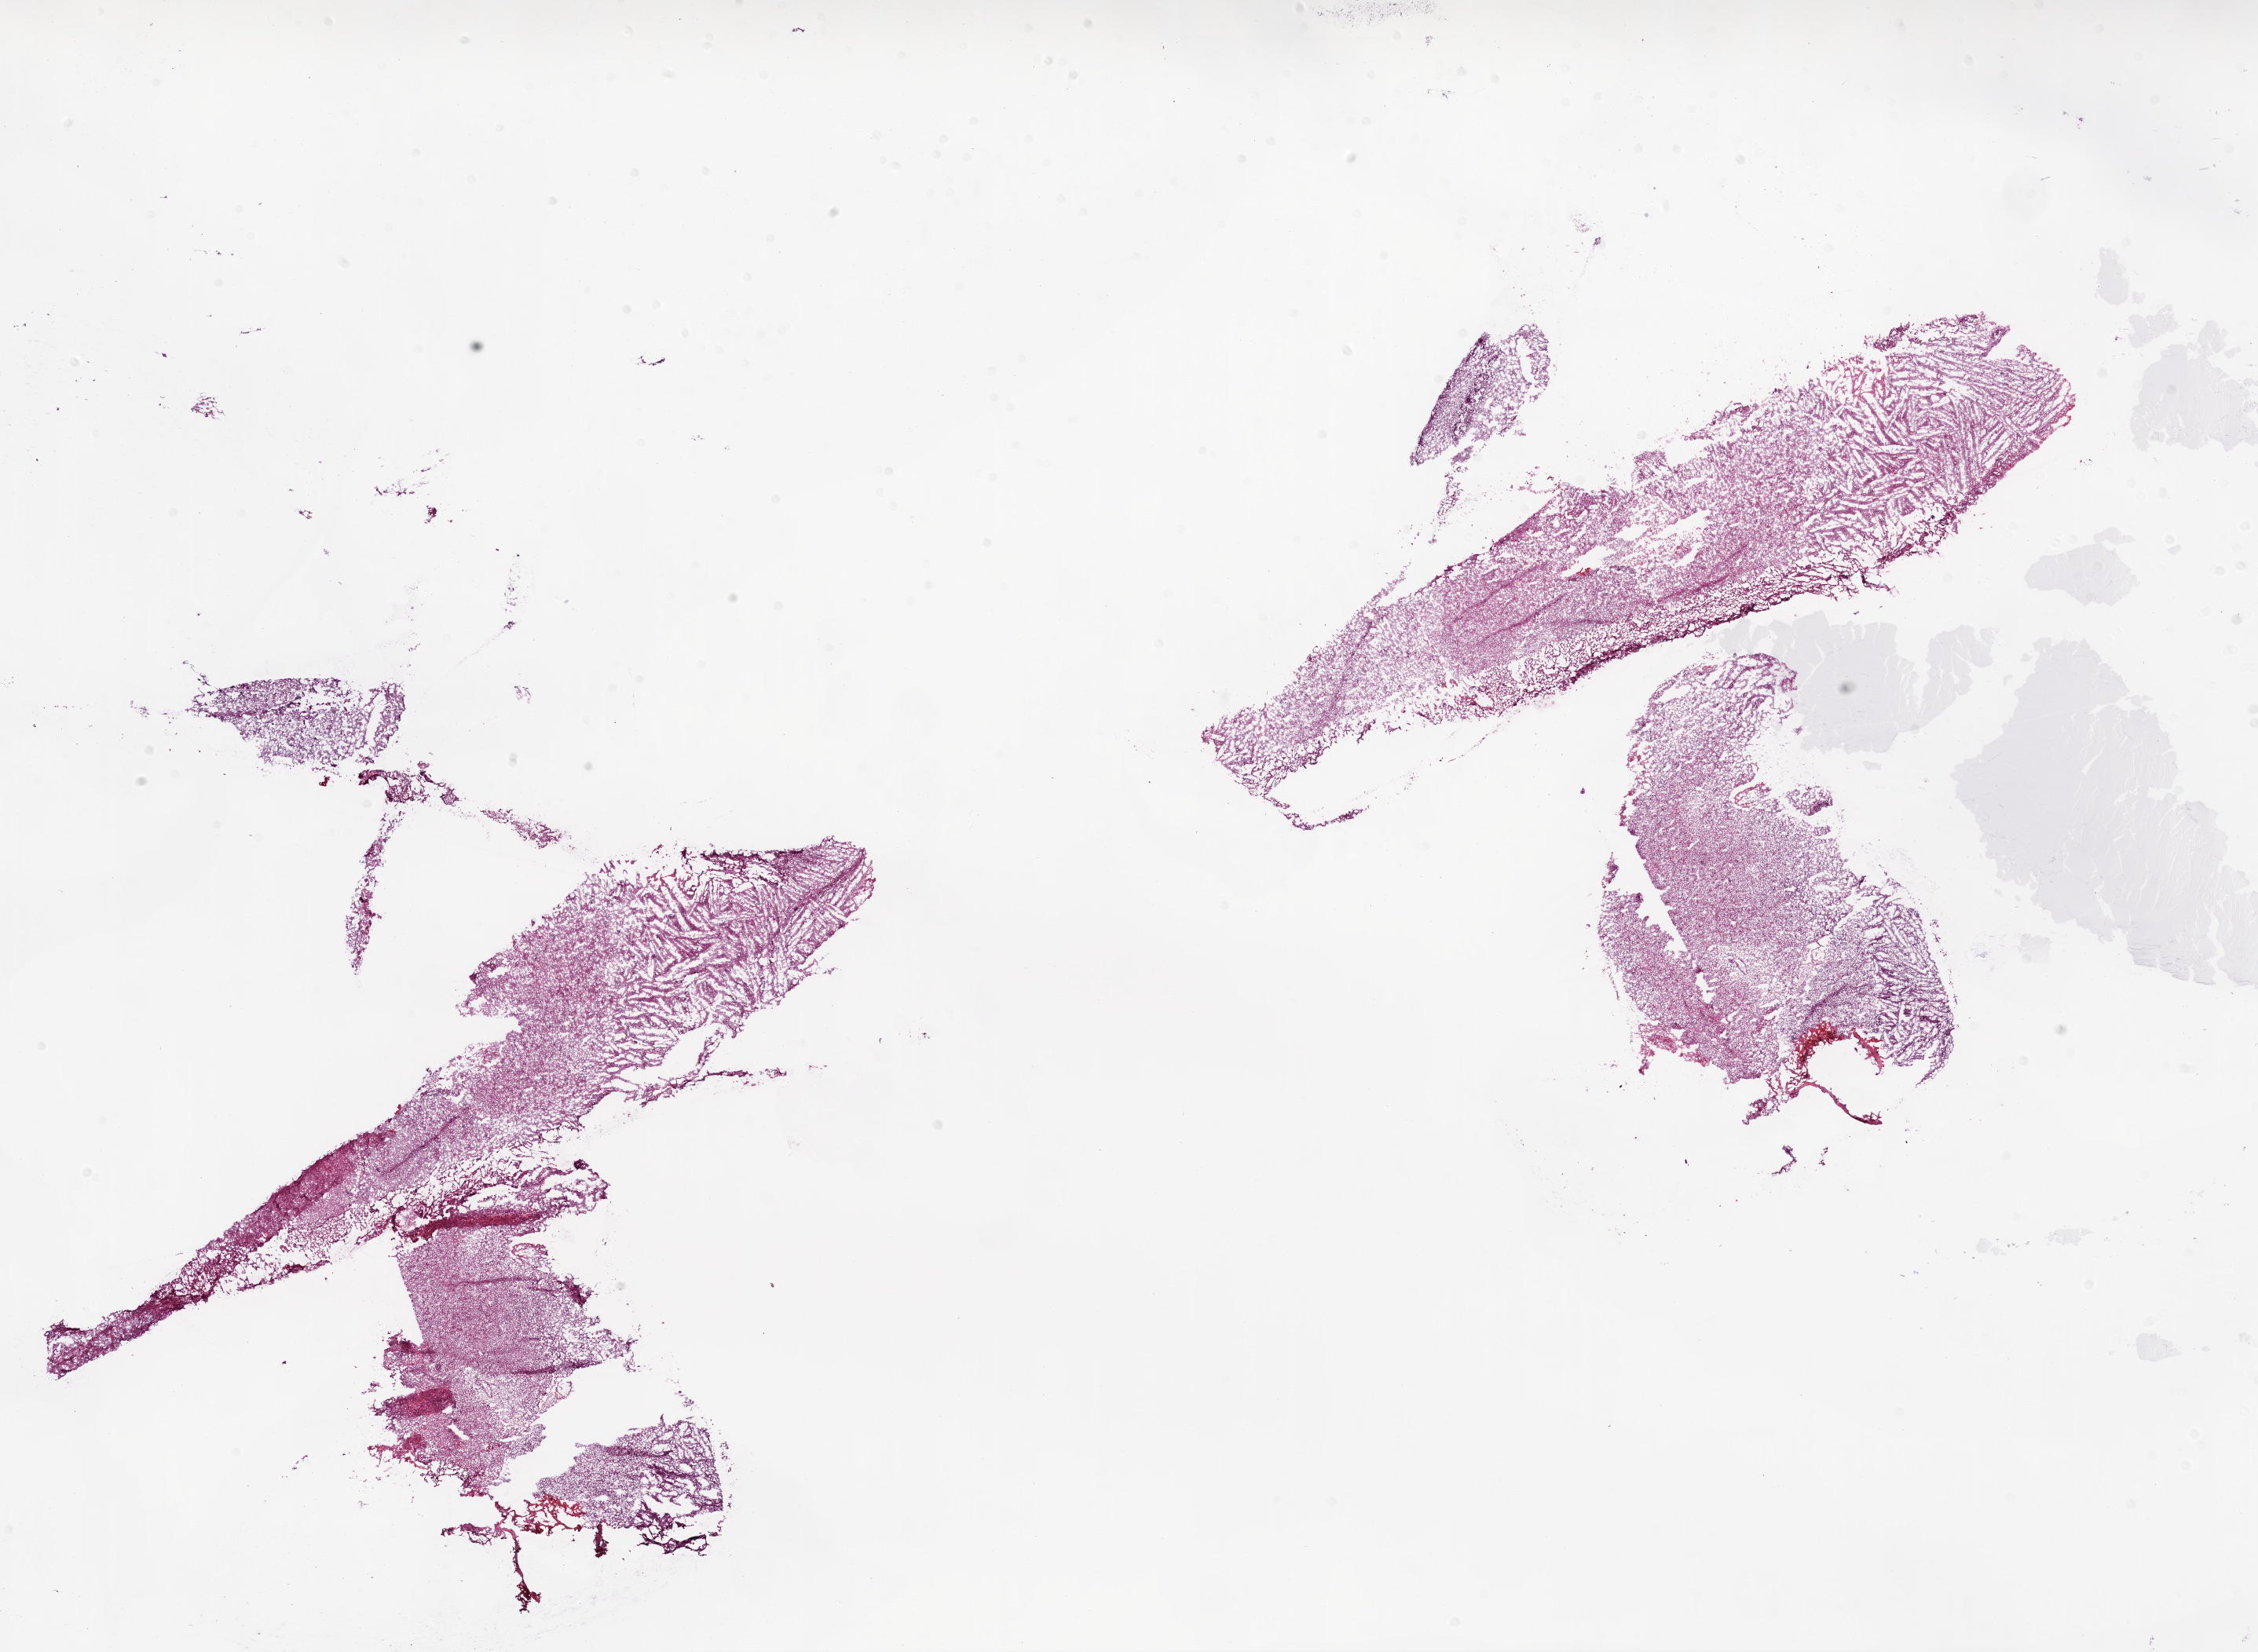
Hematoxylin and eosin (H&E) stained whole-slide image — shown as a low-resolution overview of the whole scanned area (about 23.1 x 16.9 mm). Frozen section. Primary tumour sample from the brain. Patient: male, age at initial diagnosis 65 years. Pathologist review of this section (percent, as recorded): tumour cells 100%, tumour nuclei 90%, normal cells 0%, stromal cells 0%, necrosis 0%.
• pathologic diagnosis: Glioblastoma